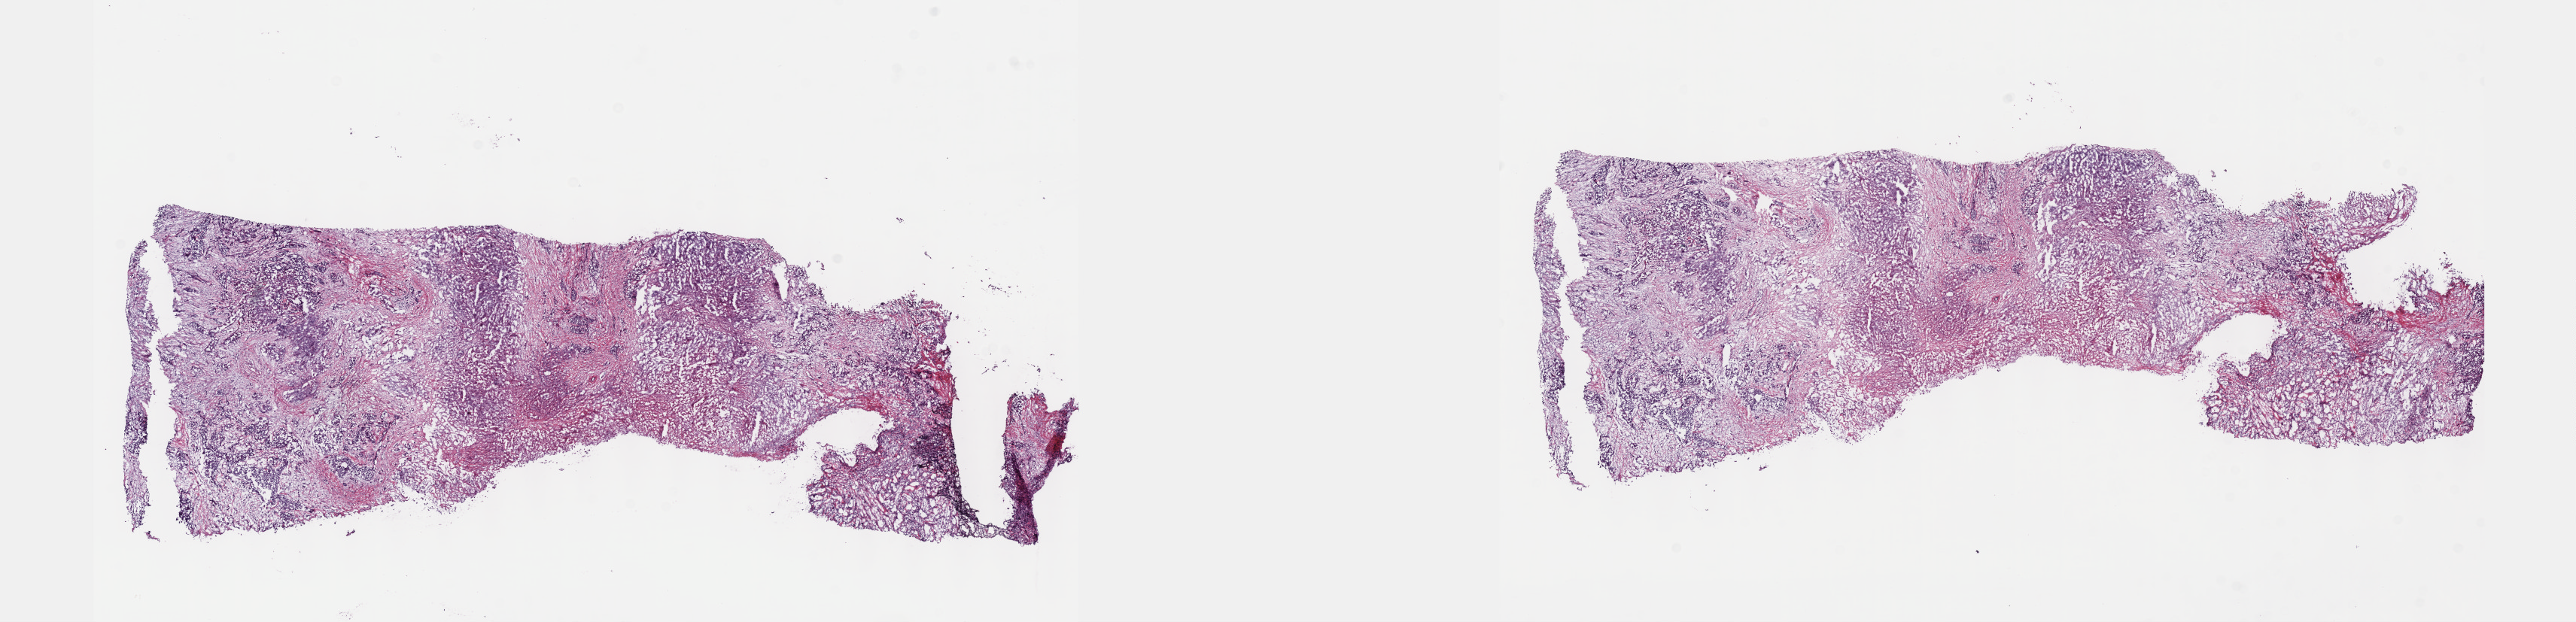
Hematoxylin and eosin (H&E) stained whole-slide image, whole scanned area (about 27.7 x 6.7 mm, from a 40x scan) shown as a low-resolution overview. Pathologist review of this section (percent, as recorded): tumour cells 65%, tumour nuclei 65%.
Specimen: frozen section from the top of the tissue portion; sample: primary tumour, bile duct.